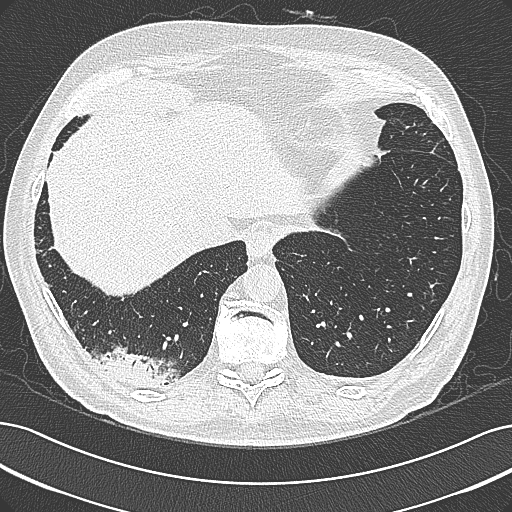
Low-dose screening chest CT, axial slice. Baseline screening round. Lung window (W 1500 / L -600 HU). 1 mm slice thickness. Lung (sharp) reconstruction kernel (B80f). 120 kVp. 512 × 512 image matrix. Male, age 68 years at enrolment.
Expert-annotated lung lesion, bounding box <96,340,187,401> (left, top, right, bottom; pixels). No non-calcified nodule or mass ≥4 mm was recorded by the screening reader at this exam. Official screen result: negative screen, significant abnormalities not suspicious for lung cancer.